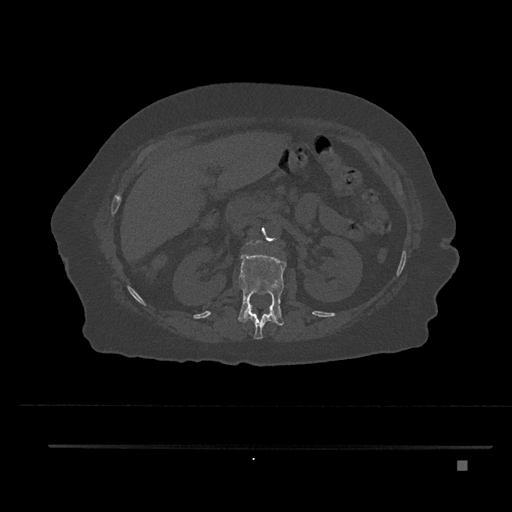
CT including the spine, one axial slice. Reconstruction kernel Br40s/3. 120 kVp. Bone window (W 1800 / L 400 HU). 0.5 mm slice thickness. 512 × 512 image matrix, field of view 437 × 437 mm. Female patient, age 76 years. Case-level facts recorded for this patient, not image findings: primary cancer: lung.
Annotated regions visible in this slice (semi-automatically segmented with operator editing):
- L1 vertebra: box from (x=238, y=252) to (x=286, y=326) px
- L2 vertebra: (x=249, y=239)–(x=259, y=246)
- T12 vertebra: (x=244, y=306)–(x=276, y=340)